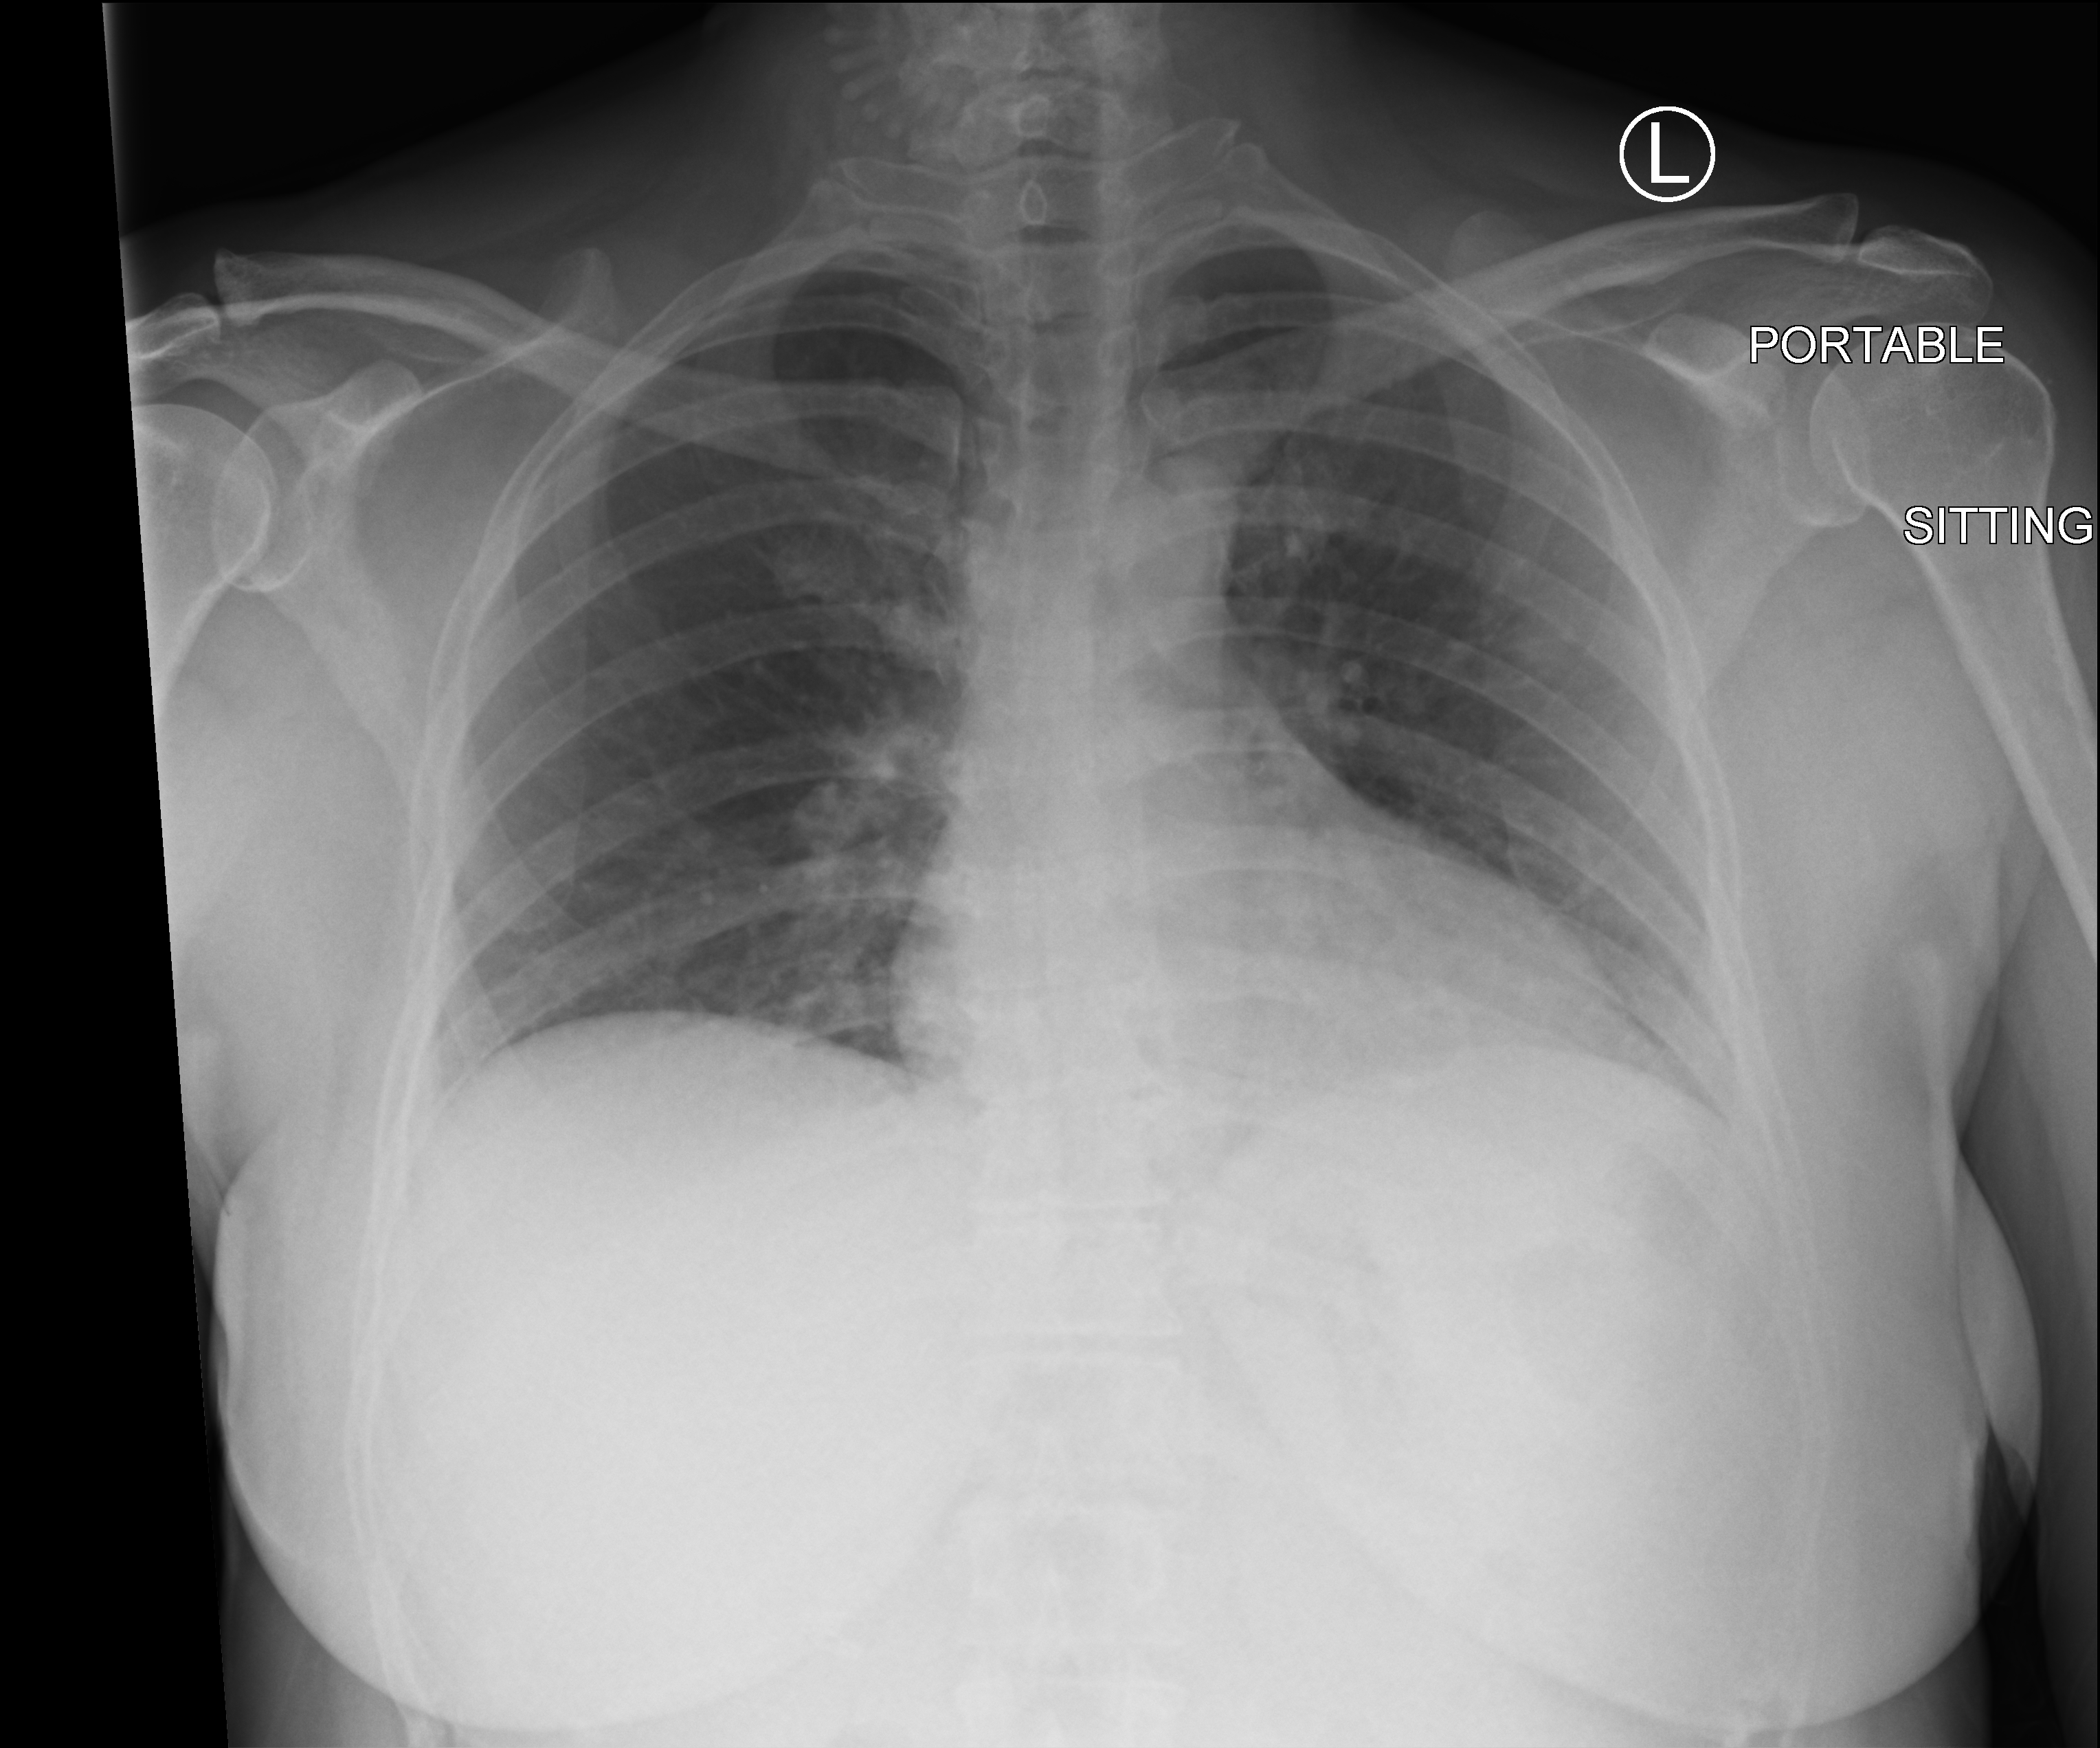
Bedside chest radiograph (computed radiography). Female patient hospitalised with COVID-19, age 18–59 years.
Admission-level facts for this patient (not findings on this image; timing relative to this image not recorded): admitted to intensive care during this hospital stay: no; mechanically ventilated during this hospital stay: no.